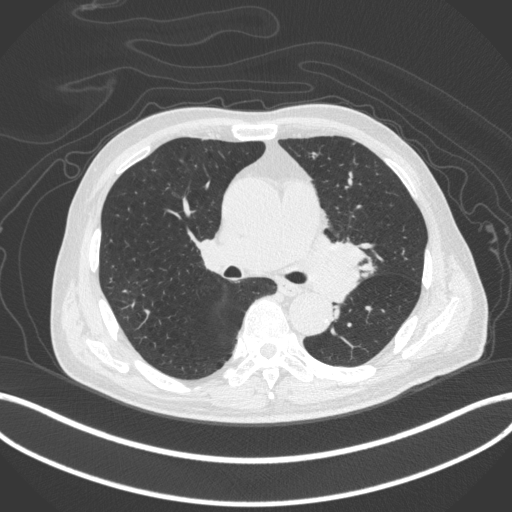
Chest CT, one axial slice; slice 254 of 420 in the series (ordered by position); reconstruction kernel B31f; 120 kVp; lung window (W 1500 / L -600 HU); 1 mm slice thickness; 512 × 512 image matrix, field of view 400 × 400 mm. Patient: male, 77 years. Case-level facts recorded for this patient, not image findings: clinical TNM (as recorded): T3 N1 M0.
Outlined on this slice (rectangle marked by the reading radiologist):
- lung tumour (recorded histology: adenocarcinoma): bounding box (x1, y1, x2, y2) in pixels: (307, 231, 378, 304)